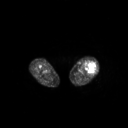
FDG PET of an extremity soft-tissue mass (from a PET/CT study), one axial slice. Position 200 of 267 along the scan axis. 128 × 128 image matrix, field of view 700 × 700 mm. Female patient, age 62 years. Case-level facts recorded for this patient, not image findings: histological type: undifferentiated – high grade; grade: high; site of the primary tumour: left thigh.
Annotated regions visible in this slice (expert contour drawn on MRI and transferred to this co-registered scan by the dataset authors):
- gross tumour volume including surrounding oedema: bounding box [x1, y1, x2, y2] px = [84, 62, 96, 74]